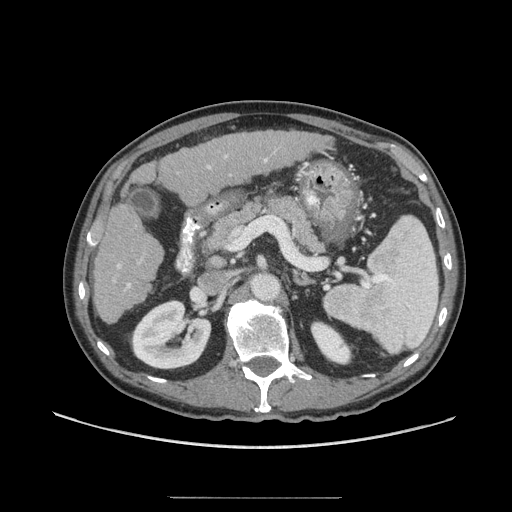
Contrast-enhanced abdominal CT (liver protocol), one axial slice. Slice 30 of 71 in the series (ordered by position). Reconstruction kernel STANDARD. 140 kVp. Soft-tissue window (W 400 / L 40 HU). 512 × 512 image matrix, field of view 400 × 400 mm. From the clinical record (not read from this slice): diagnosis: hepatocellular carcinoma (patient treated with transarterial chemoembolisation; whether this scan precedes or follows treatment is not stated here); TNM stage (as recorded): Stage-I; Child-Pugh class: A; tumour differentiation: well differentiated; tumour nodularity: uninodular.
Outlined on this slice (semi-automatic segmentation, software-assisted and operator-edited):
- liver parenchyma outside the tumour (the mass and vessels are separate outlines, so this box may not span the whole liver): bounding box <93,130,328,324> (left, top, right, bottom; pixels)
- liver vessels: <114,155,268,288>